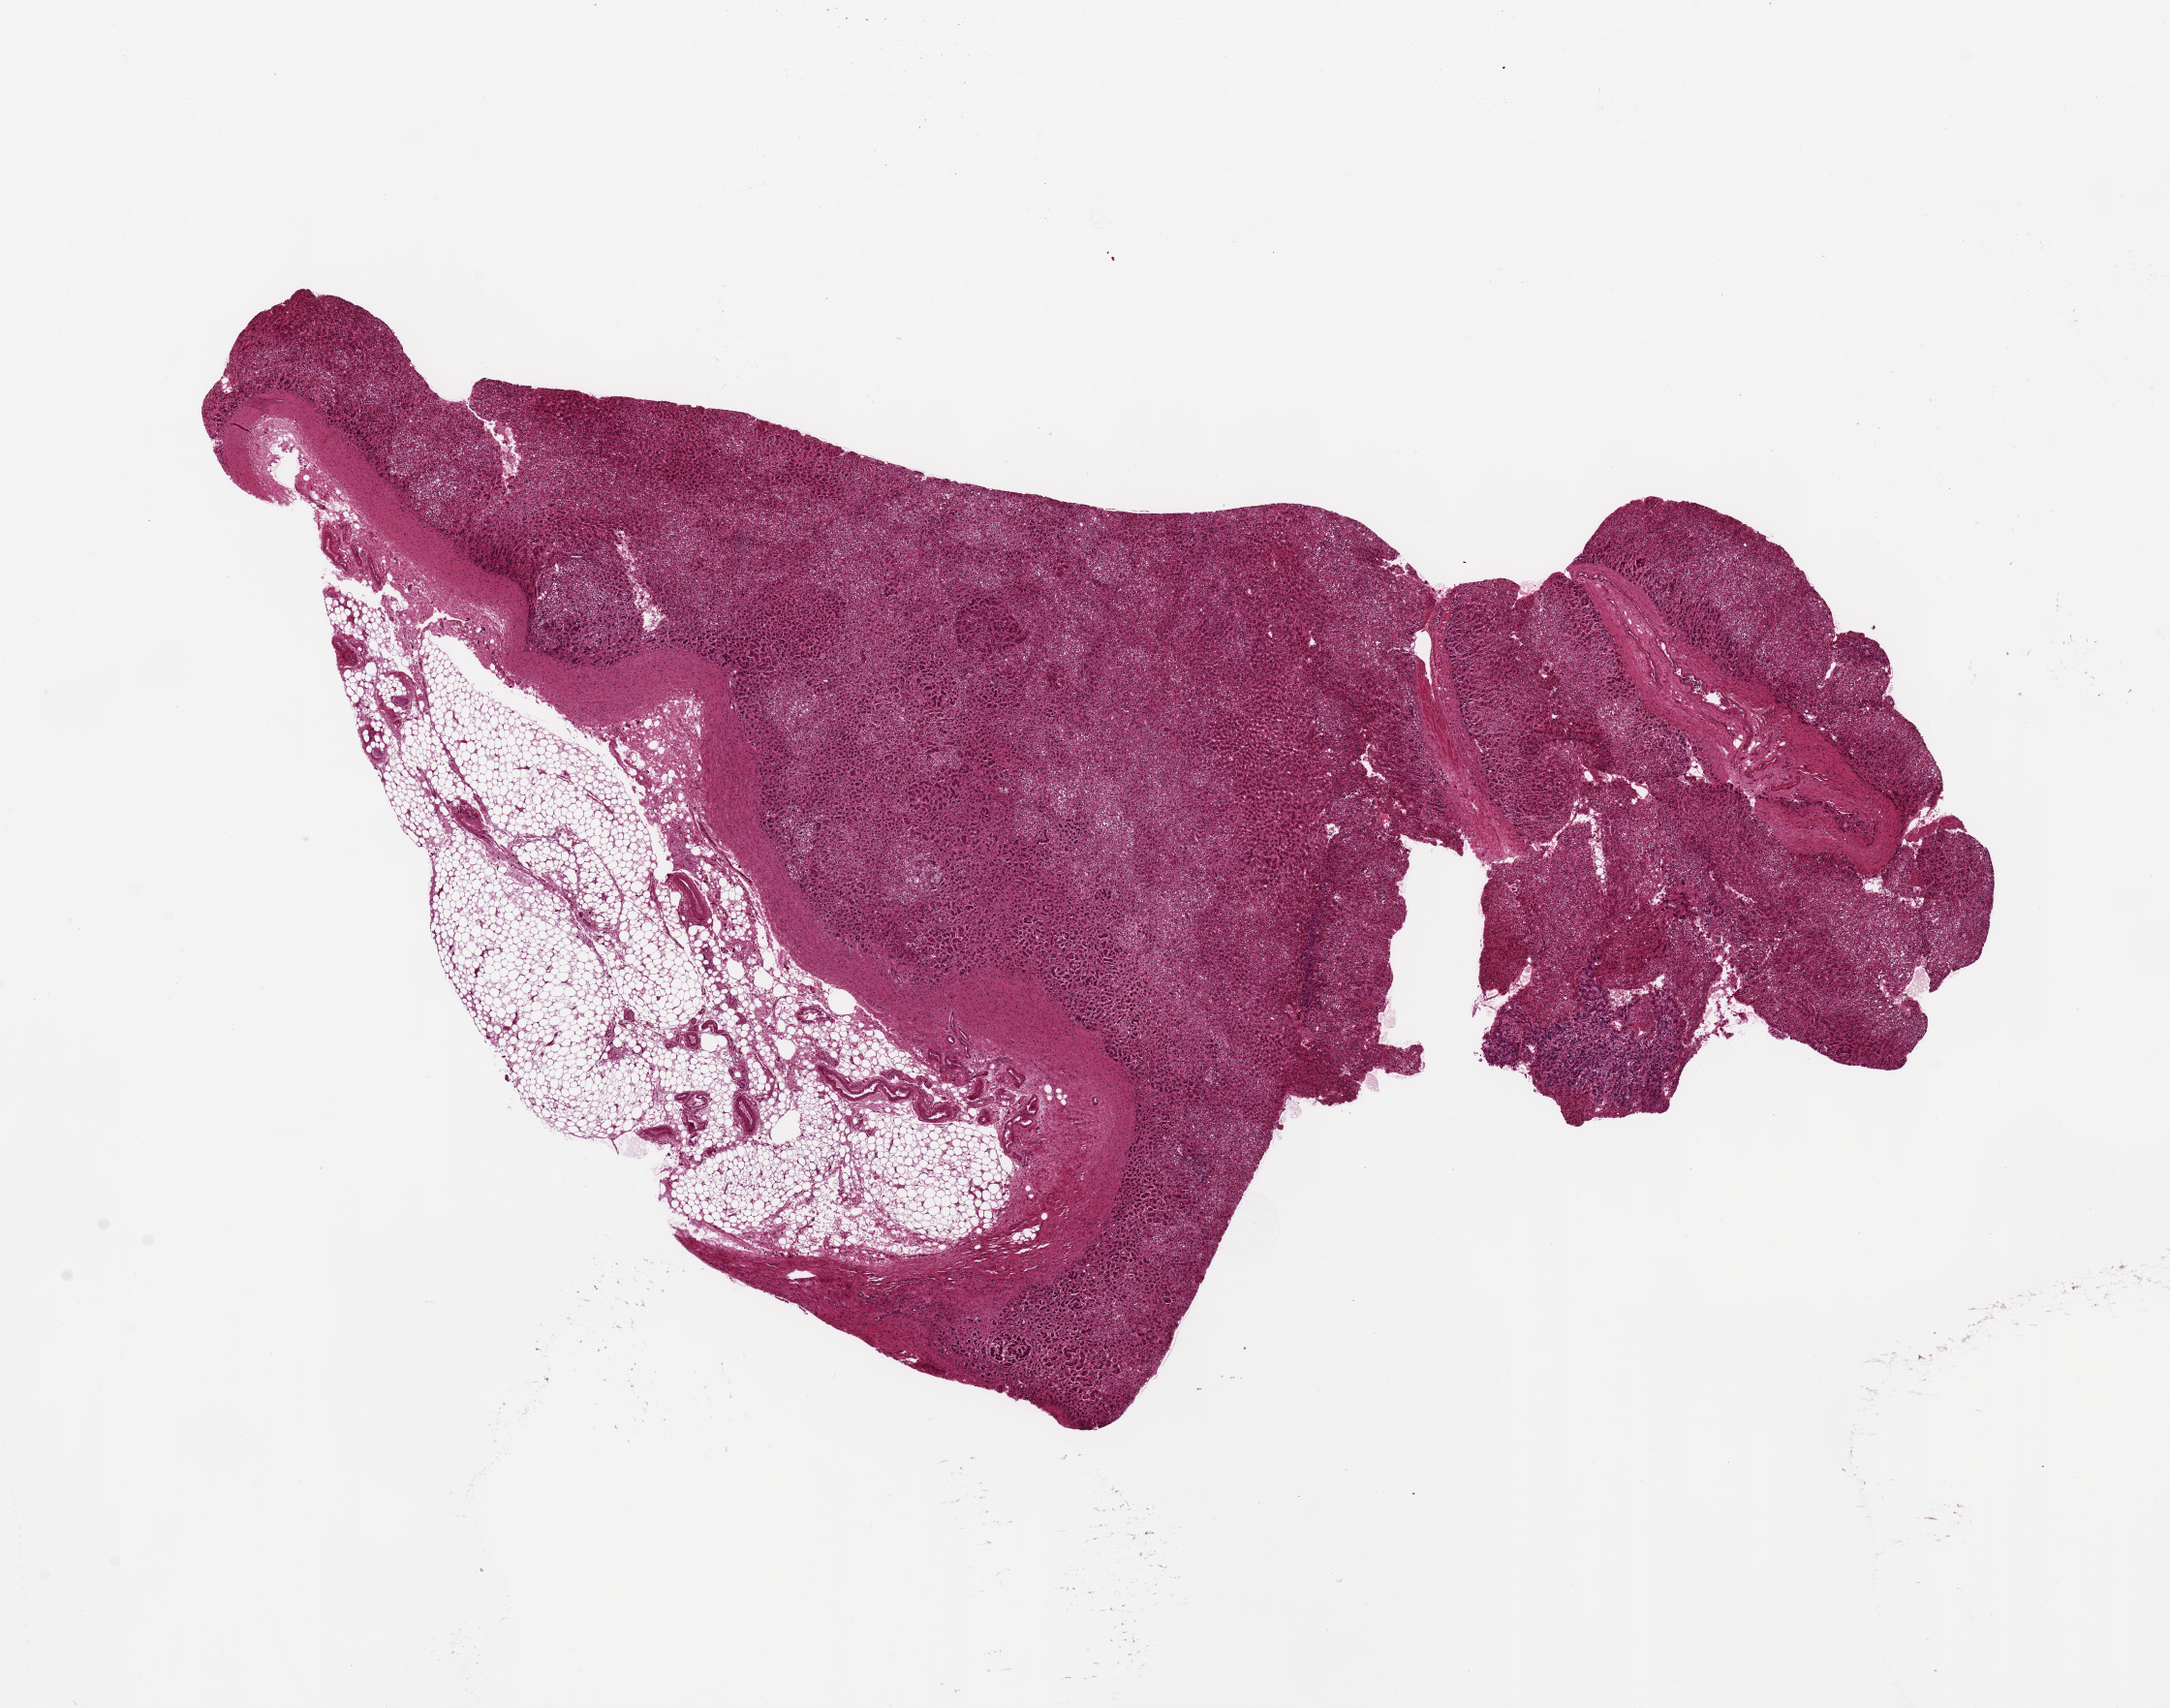
Digitized haematoxylin and eosin-stained section — low-resolution overview of the scanned area, about 17.7 x 13.9 mm (from a 20x scan), PAXgene-fixed paraffin-embedded (PFPE) section, target tissue: adrenal gland, donor tissue sample. Donor sex: male.
Reviewer comment on this tissue sample: focally autolysis is 3; 11.5x11mm. 6x2.4mm nubbin of fat on one edge.